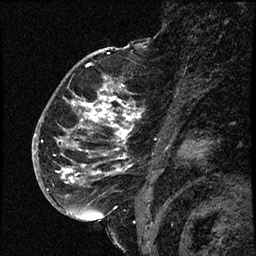
Breast MRI (dynamic contrast-enhanced), one sagittal slice; position 41 of 66 along the scan axis; dynamic contrast-enhanced study with each time point stored as its own series, time point 2 of 3 at this slice position (early post-contrast, ordered by acquisition time); 1.5 T; TE 4.2 ms, TR 17.6 ms; 2 mm slice thickness; 256 × 256 image matrix, field of view 200 × 200 mm. Female patient. From the clinical record (not read from this slice): setting: breast cancer imaged before/during neoadjuvant chemotherapy; receptor status: HER2-positive.
Outlined on this slice (semi-automatically segmented with operator editing):
- analysis volume of interest (the breast-tissue region the enhancement analysis was run in; not a lesion): bounding box (x1, y1, x2, y2) in pixels: (52, 69, 146, 209)
- tumour enhancement mask (voxels above the 100 % enhancement threshold inside the analysis volume of interest): (58, 91, 140, 181)